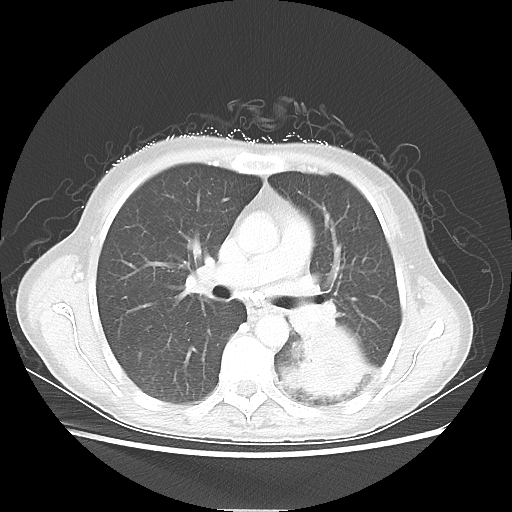
Chest CT, one axial slice. Slice 33 of 56 in the series (ordered by position). Reconstruction kernel LUNG. Lung window (W 1500 / L -600 HU). 5 mm slice thickness. 512 × 512 image matrix, field of view 360 × 360 mm. Patient: female, 53 years. From the clinical record (not read from this slice): clinical TNM (as recorded): T3 N0 M0.
Structures marked on this image (rectangle marked by the reading radiologist):
- lung tumour (recorded histology: adenocarcinoma): box from (x=276, y=326) to (x=378, y=402) px